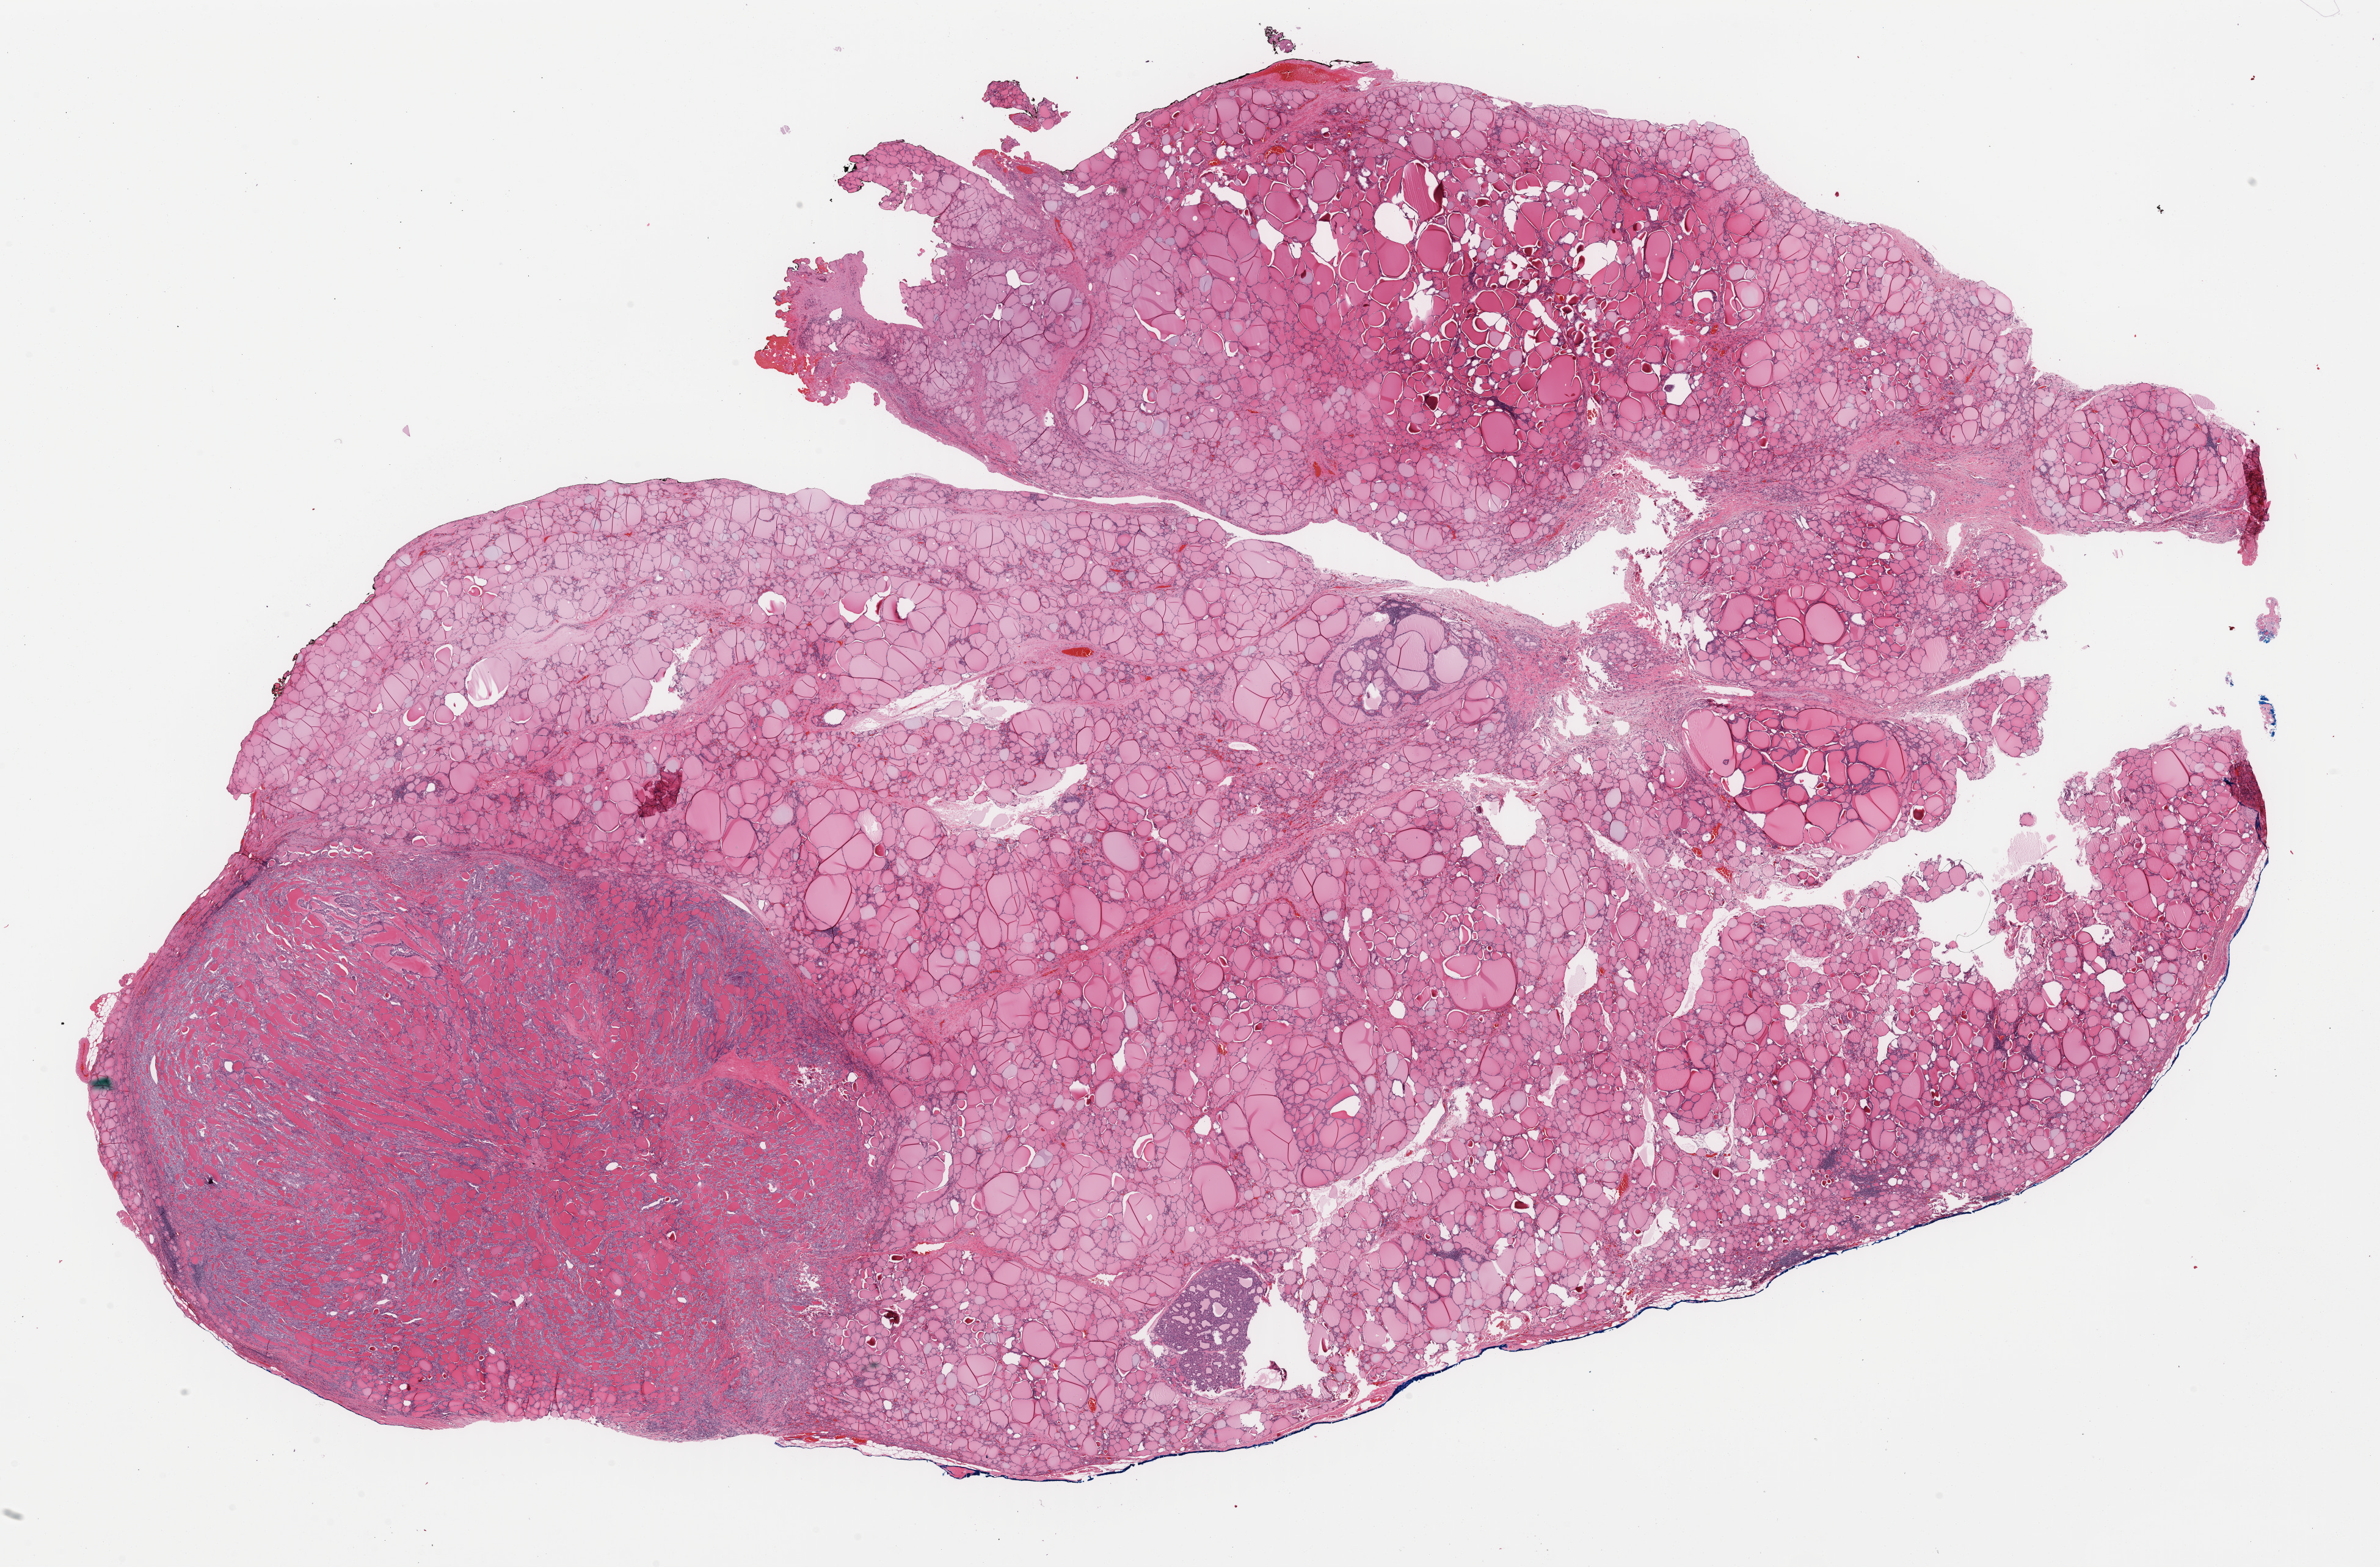
Whole-slide histology image, H&E — whole scanned area (about 30.7 x 20.2 mm) shown as a low-resolution overview. Formalin-fixed paraffin-embedded (FFPE) diagnostic section. Sample: primary tumour, thyroid. Female, age 70 years at initial diagnosis.
Histologic diagnosis: Papillary adenocarcinoma, NOS (thyroid gland). AJCC pathologic stage: III (7th edition). Laterality: bilateral.